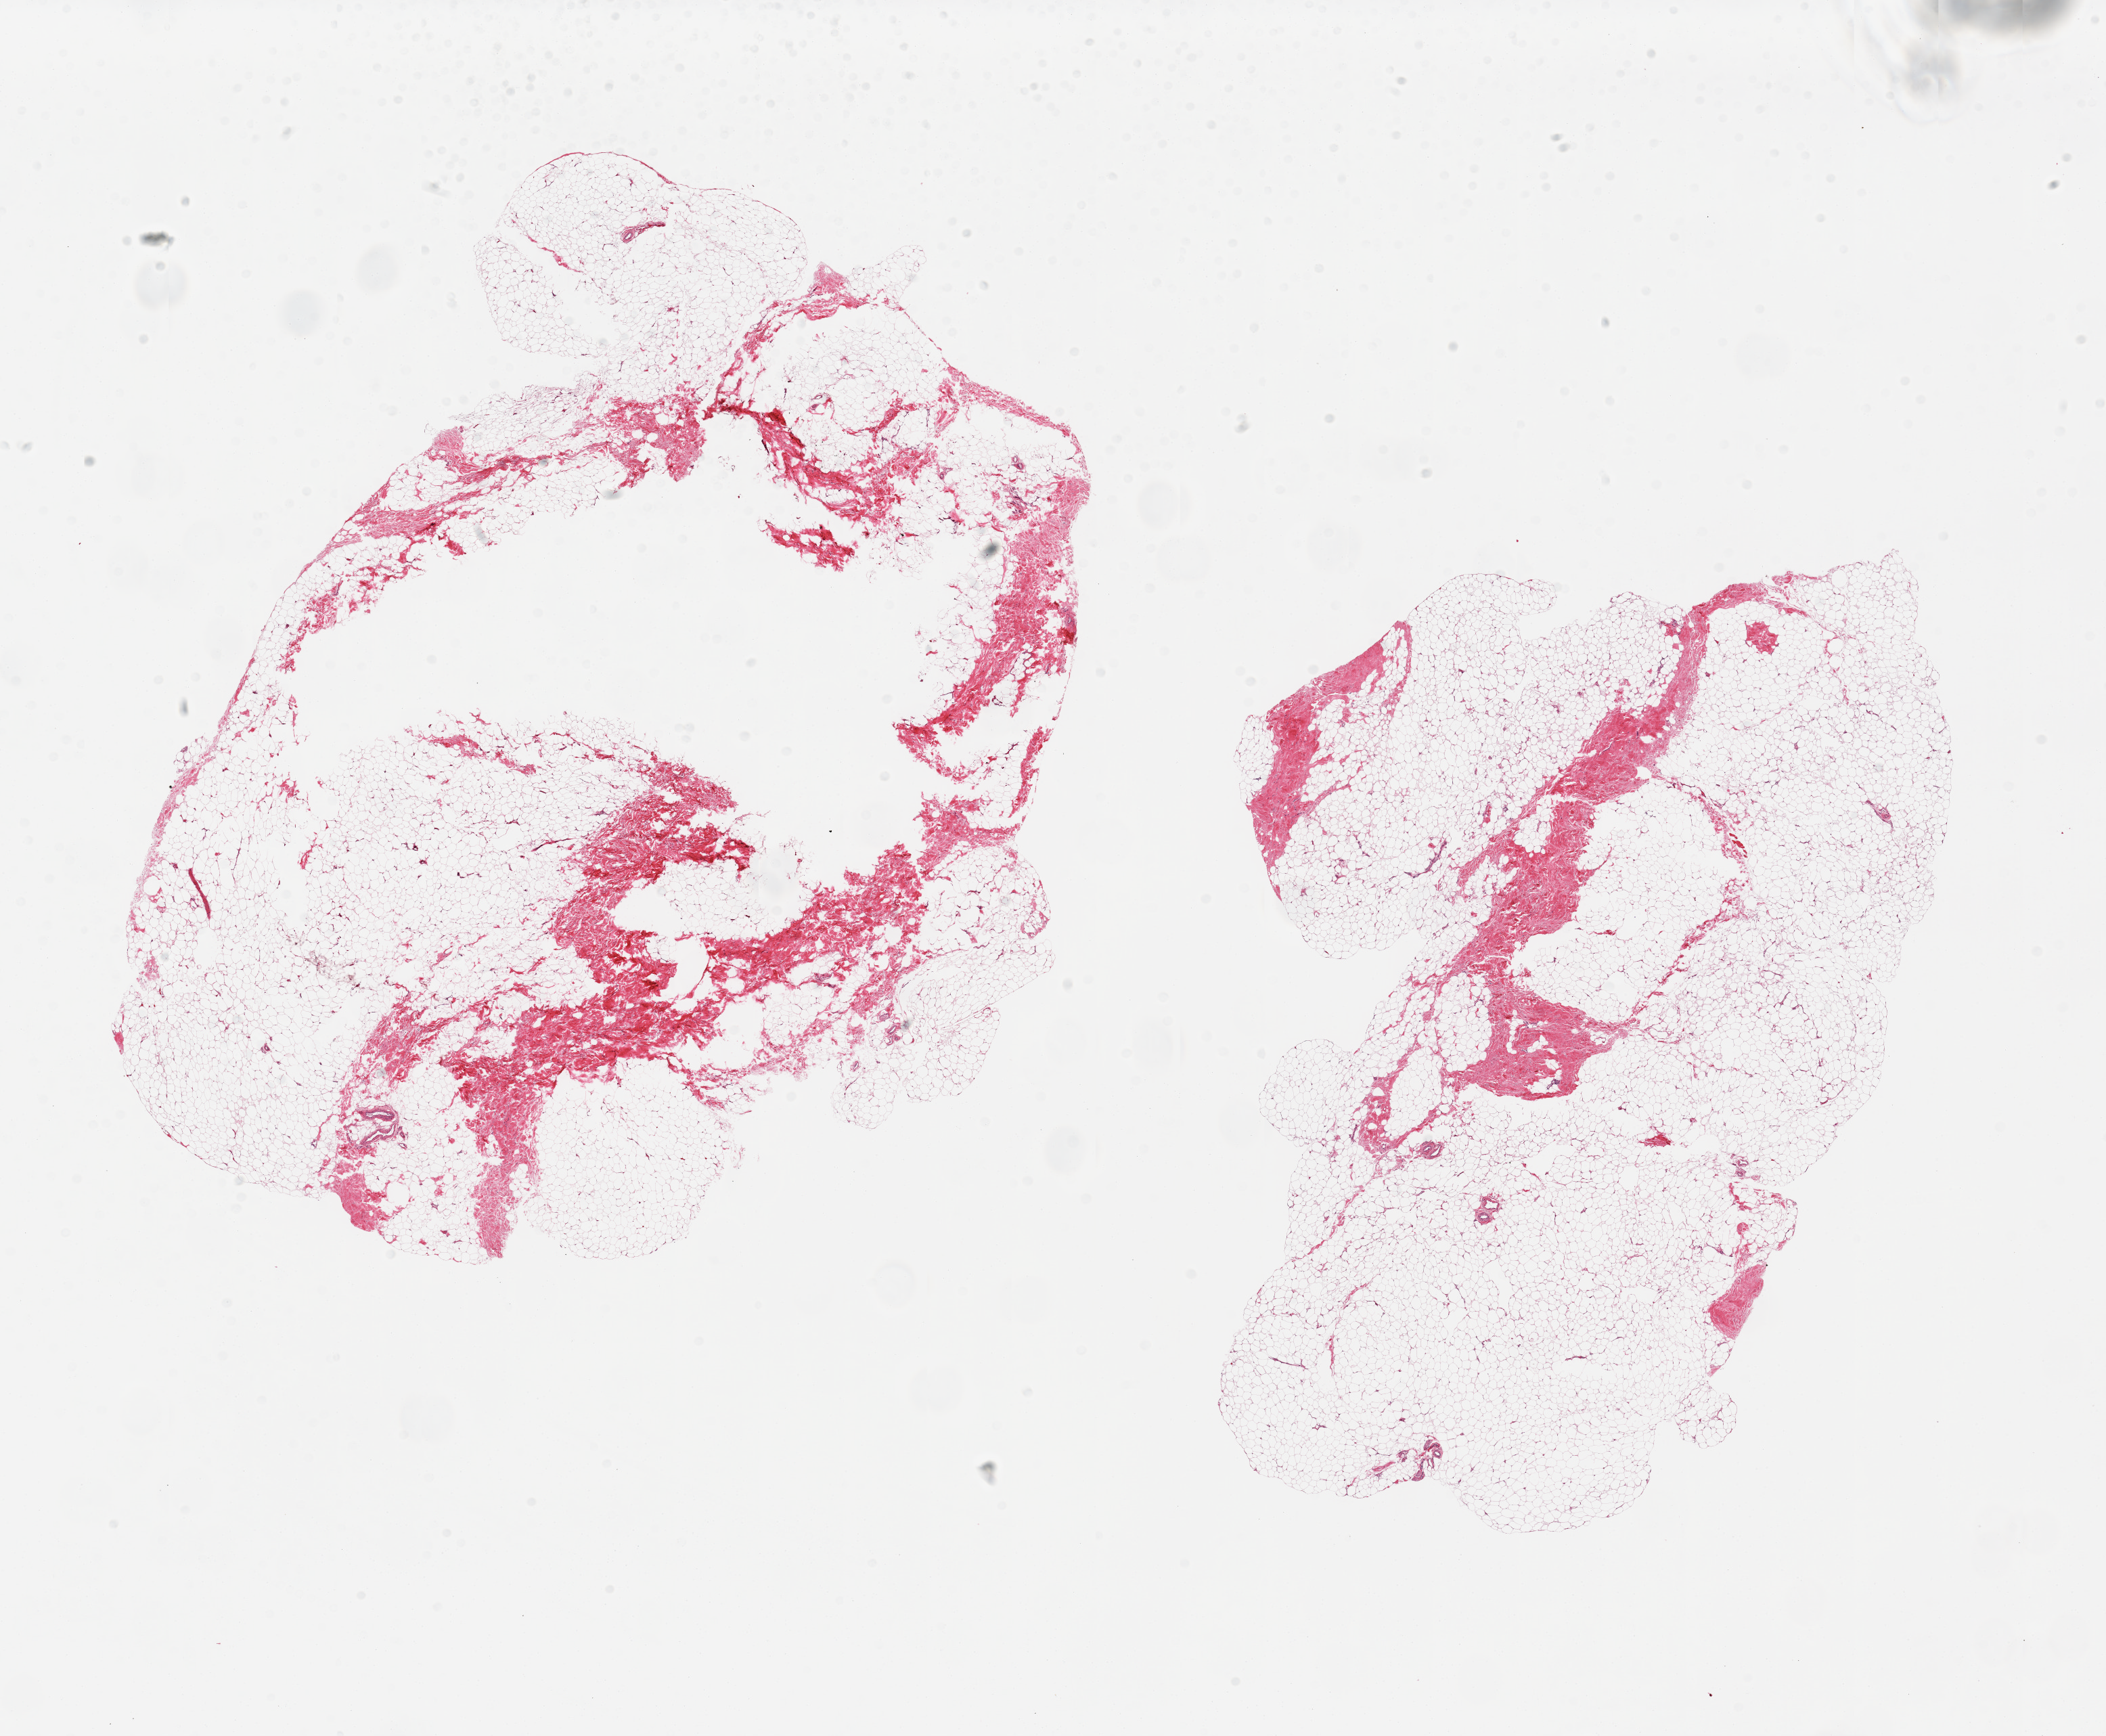
Whole-slide image, H&E stain, a low-resolution overview of the entire scanned area, about 24.6 x 20.3 mm. PAXgene-fixed paraffin-embedded (PFPE) section. Section of breast (target tissue). Donor tissue sample. Donor: male.
Pathologist's review note for this sample: 2 pieces; fibrofatty tissue, no ducts; large hole in 1 piece.